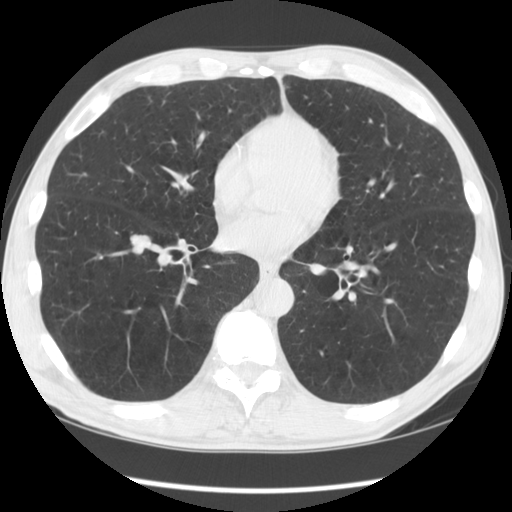
Axial slice from a low-dose chest CT screening exam, second annual screen, lung window (W 1500 / L -600 HU), 2.5 mm slice thickness, 120 kVp, slice 86 of 135 in the series. Male participant, aged 60 years at enrolment. Current smoker at enrolment.
Expert reader's lesion annotation, box from (x=112, y=225) to (x=159, y=267) px. Reader record for this screening exam (exam-level; its link to the box is not recorded): non-calcified nodule or mass ≥4 mm, right lower lobe, 17 × 14 mm, smooth margins, soft tissue attenuation, pre-existing on the prior screen: yes; interval growth: yes. Official screen result: positive, other. Later outcome: lung cancer diagnosed 39 days after this screen — large cell carcinoma, NOS, right lower lobe, undifferentiated (G4), stage IA (AJCC 6th edition), 16 mm at pathology.